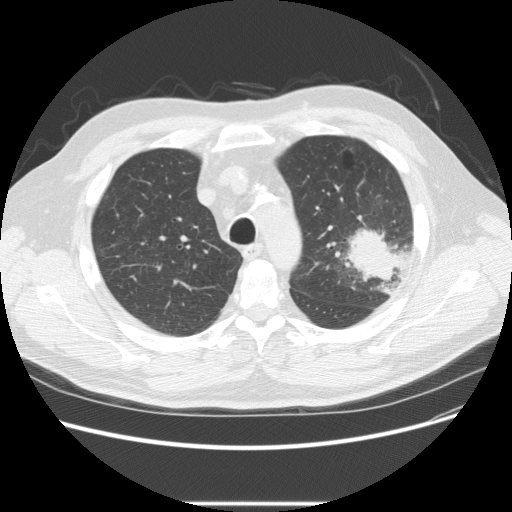
Chest CT (low-dose screening protocol), one axial image, first (baseline) screen, lung window (W 1500 / L -600 HU), 2.5 mm slice thickness, 512 × 512 image matrix, field of view 380 × 380 mm. Male, age 73 years at enrolment. Former smoker at enrolment.
Lesion marked by an expert reader, bounding box [x1, y1, x2, y2] px = [332, 215, 415, 286]. The screening reader recorded 2 non-calcified nodules or masses ≥4 mm on this exam (left upper lobe, right upper lobe); which of them this box marks is not recorded. Participant outcome: lung cancer diagnosed 11 days after this screen — bronchiolo-alveolar adenocarcinoma, NOS, other location, well differentiated (G1), stage IV (AJCC 6th edition).